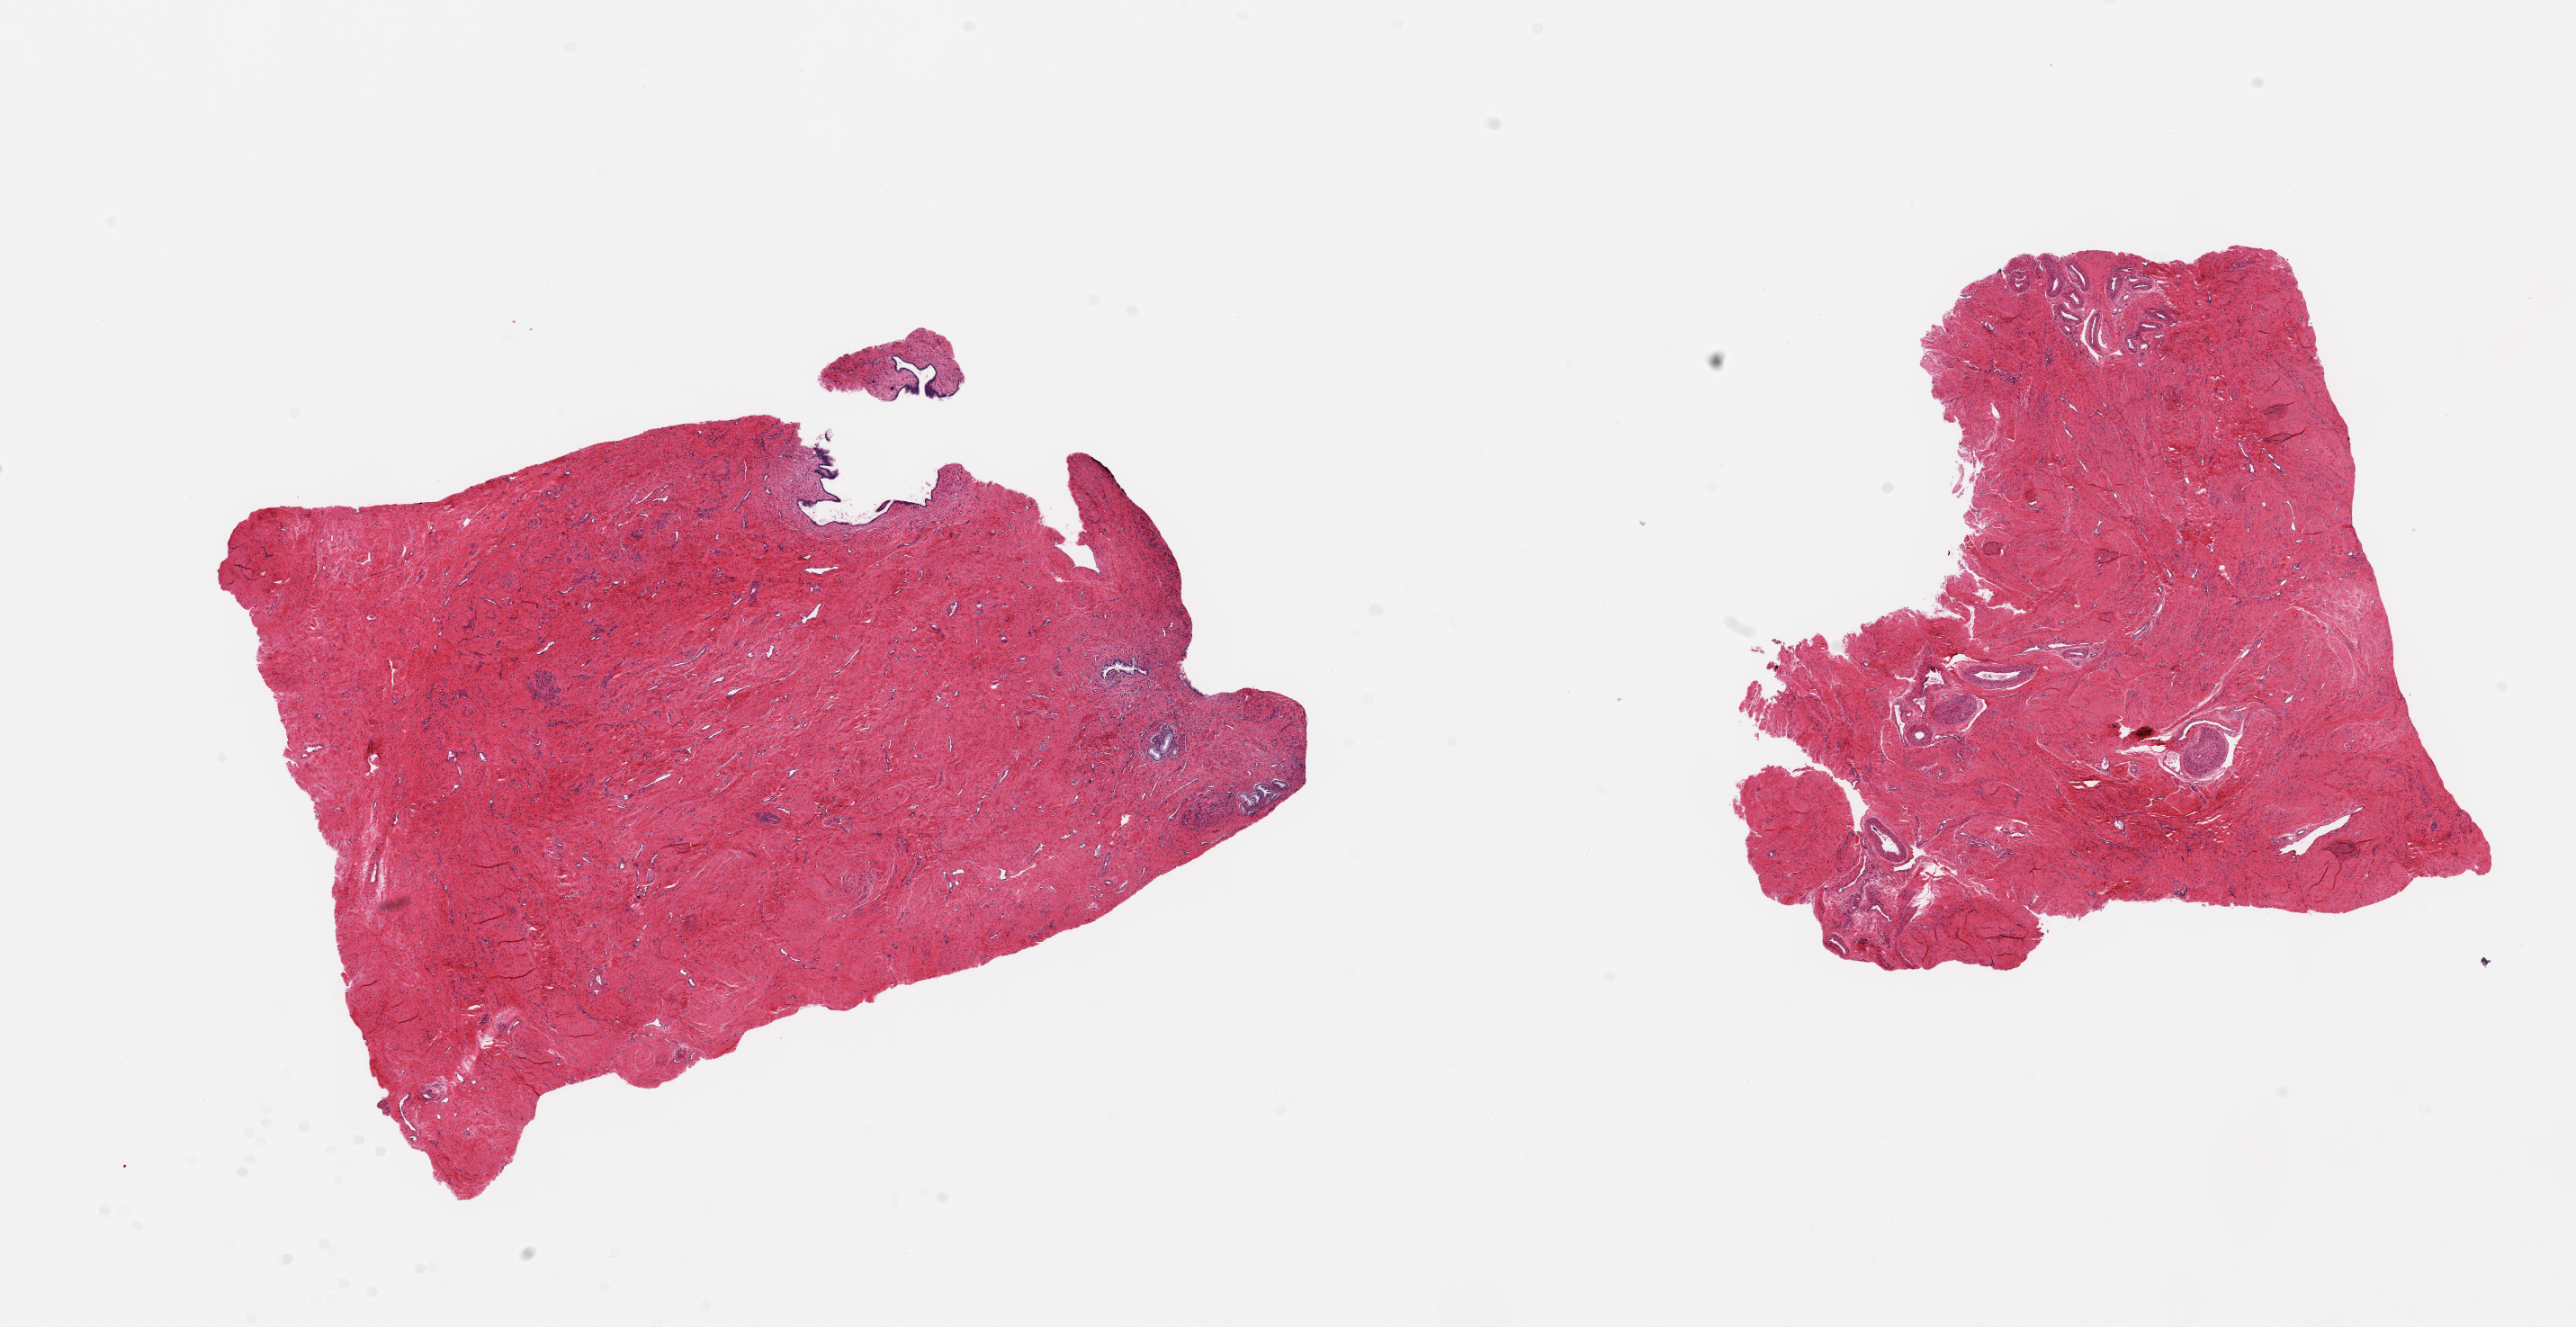
H&E whole-slide image, a low-resolution overview of the entire scanned area, about 22.6 x 11.7 mm. PAXgene-fixed, paraffin-embedded tissue. Section of endocervix (target tissue). Tissue donor sample. Female donor.
Pathologist's review note for this sample: 2 ~8x6mm pieces. One has a few 0.2-0.3mm glands, fairly well preserved but less than 0.5% of total specimen.